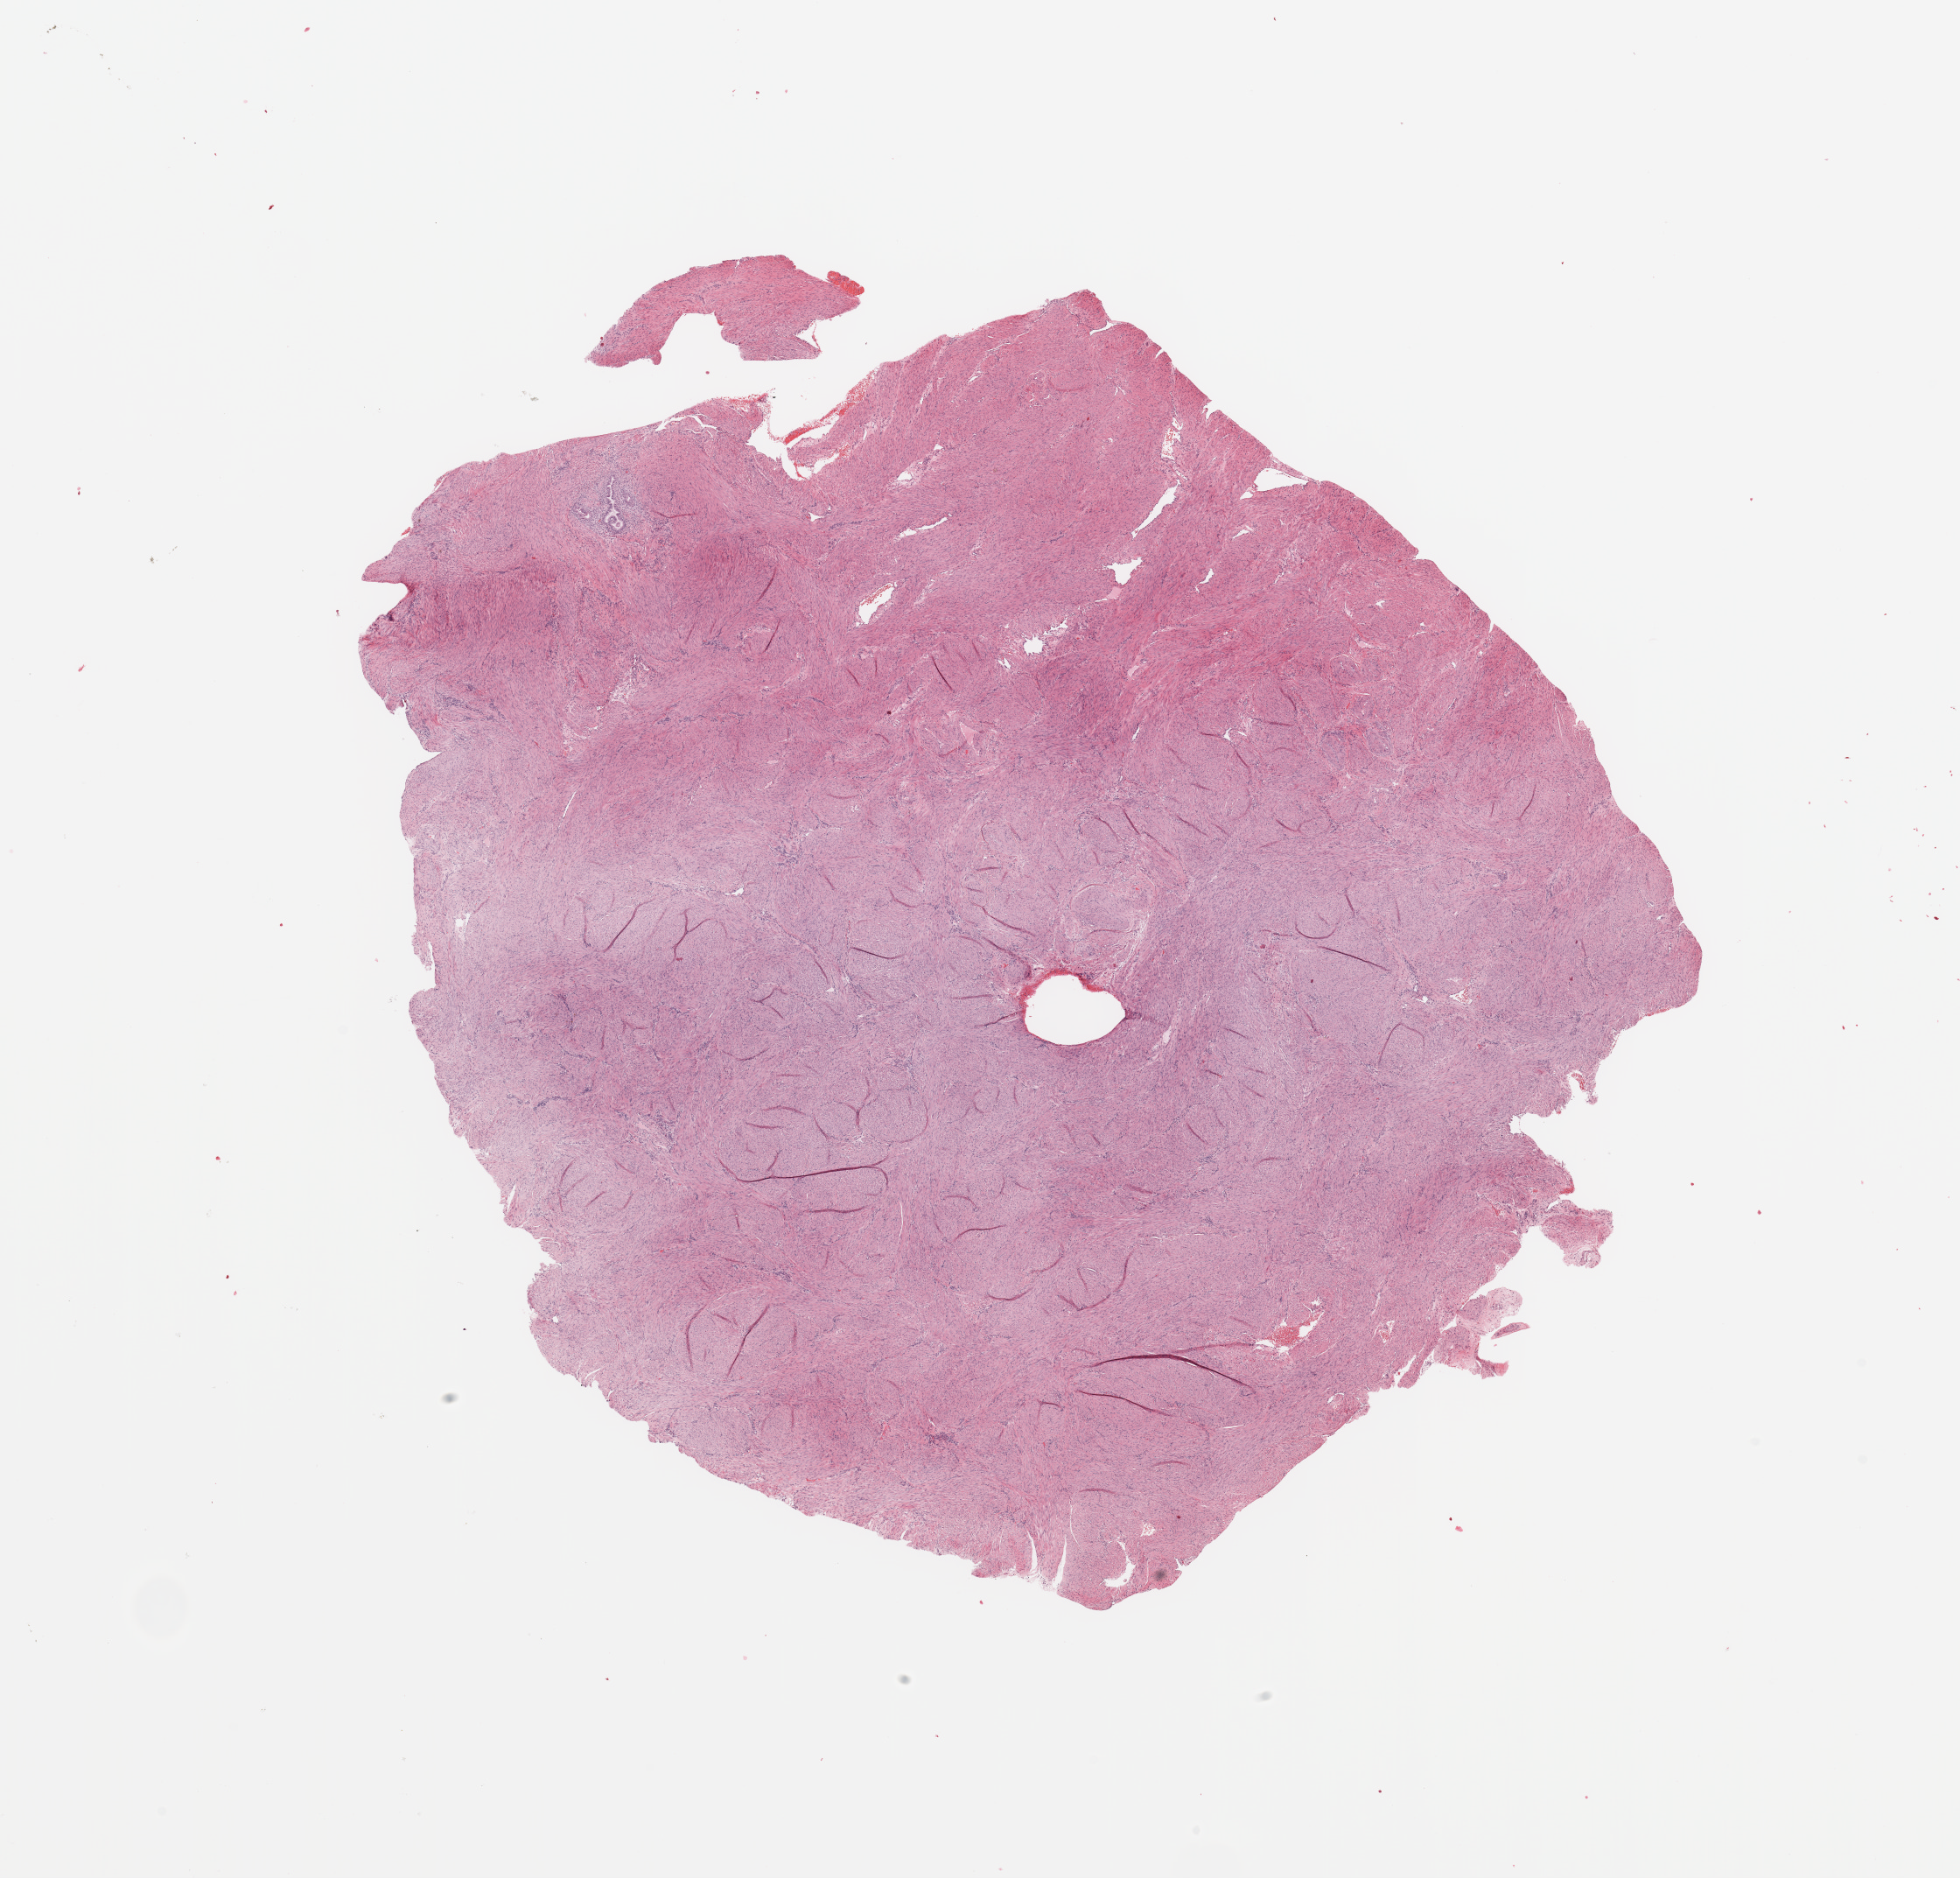
H&E-stained whole-slide image — low-resolution overview of the scanned area, about 17.7 x 17.0 mm (acquisition: 20x scan). Normal (non-tumour) tissue sample, uterus. 58-year-old female patient.
This section: normal (non-tumour) tissue from the same patient. Patient diagnosis: Endometrioid adenocarcinoma, NOS.